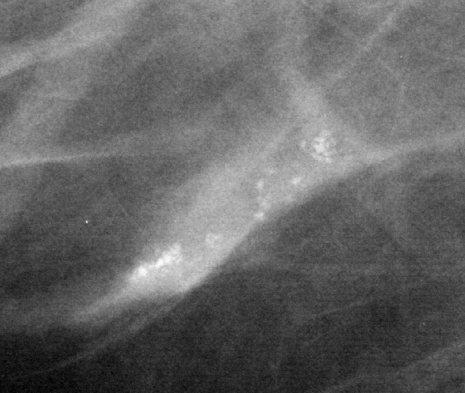
Region of interest cut from a scanned film mammogram (one marked finding); right breast; MLO view; BI-RADS breast density category 2 (scale 1–4).
- Calcifications, morphology pleomorphic, distribution clustered; BI-RADS assessment category 4; pathology result (as recorded, not read from the image): benign.